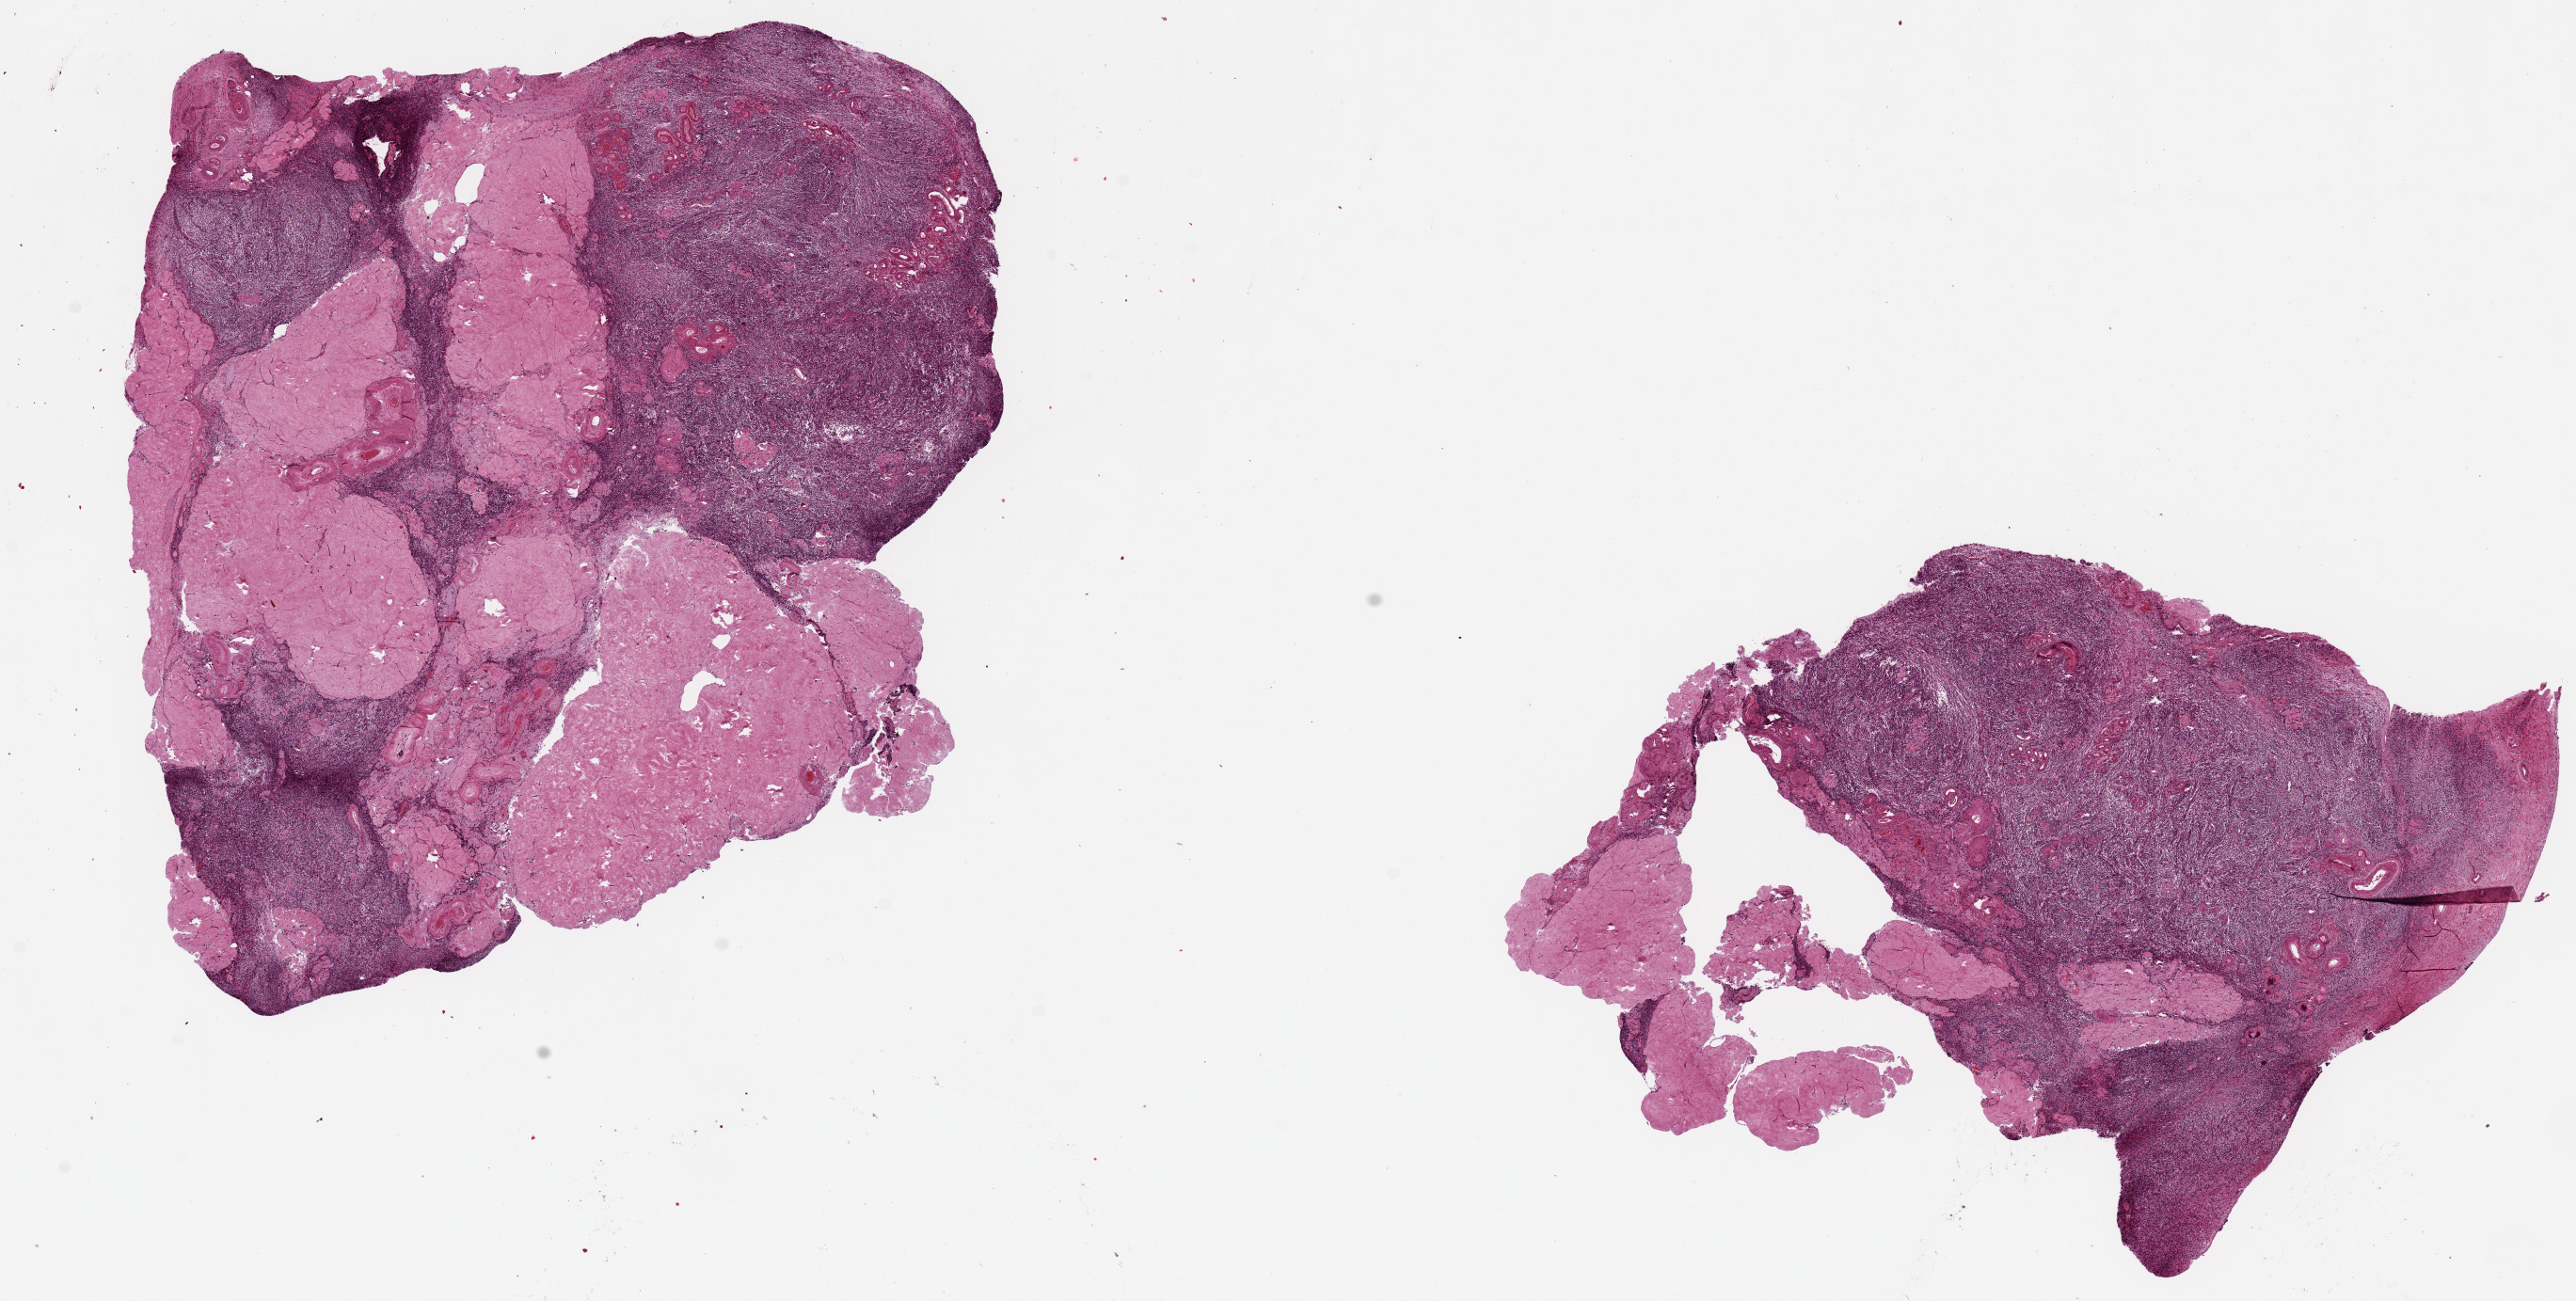
Hematoxylin and eosin (H&E) whole-slide image, brightfield, shown as a low-resolution overview of the whole scanned area (about 21.7 x 10.9 mm, from a 20x scan); PAXgene-fixed, paraffin-embedded tissue; section of ovary (target tissue); donor tissue sample. Female donor.
Pathologist's review note for this sample: 2 pieces, 8x7 & 7x6mm; ~50% corpora ablicantia.